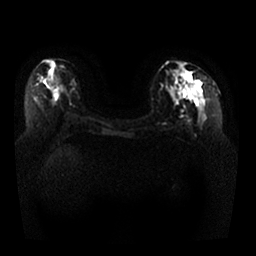
Breast MRI, one axial slice; diffusion-weighted series; image 2 of 4 stored at this slice position (different b-values; order by instance number); 1.5 T; 256 × 256 image matrix, field of view 350 × 350 mm. Female patient.
Annotated regions visible in this slice (manually delineated by an expert):
- tumour on diffusion-weighted imaging: box from (x=177, y=86) to (x=193, y=99) px